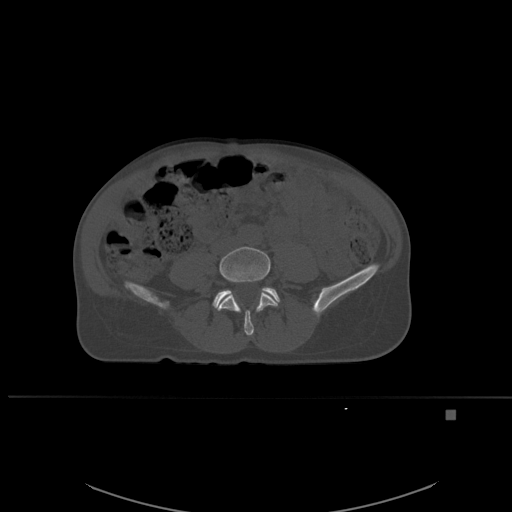
CT including the spine, one axial slice; slice 185 of 537 in the series (ordered by position); bone window (W 1800 / L 400 HU); 512 × 512 image matrix, field of view 440 × 440 mm. Female patient, age 45 years. From the clinical record (not read from this slice): primary cancer: lung.
Structures marked on this image (semi-automatic segmentation, software-assisted and operator-edited):
- L4 vertebra: bounding box [x1, y1, x2, y2] px = [213, 246, 278, 336]
- L5 vertebra: [213, 287, 280, 306]